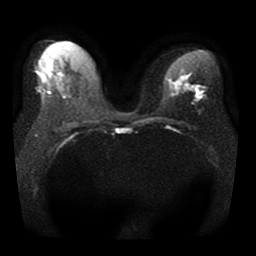
Breast MRI, one axial slice. Slice 20 of 41 in the series (ordered by position). Diffusion-weighted series; image 2 of 4 stored at this slice position (different b-values; order by instance number). 1.5 T. 5 mm slice thickness. 256 × 256 image matrix. Female patient.
Outlined on this slice (outlined manually by an expert reader):
- tumour on diffusion-weighted imaging: bounding box <196,88,202,94> (left, top, right, bottom; pixels)